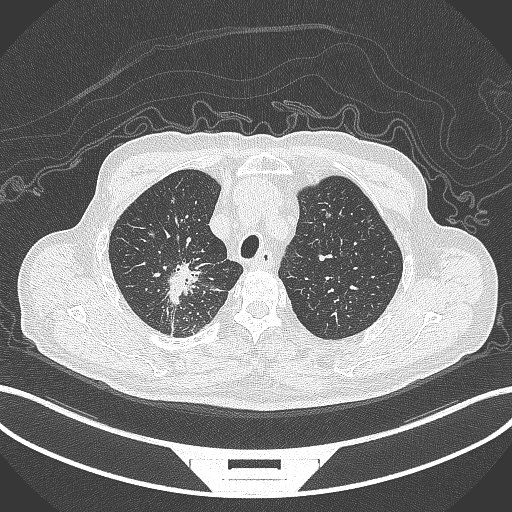
Chest CT, one axial slice; slice 305 of 407 in the series (ordered by position); reconstruction kernel B70f; lung window (W 1500 / L -600 HU); 1 mm slice thickness; 512 × 512 image matrix, field of view 400 × 400 mm. Male patient, age 69 years. Case-level facts recorded for this patient, not image findings: clinical TNM (as recorded): T1c N1 M1.
Annotated regions visible in this slice (rectangle marked by the reading radiologist):
- lung tumour (recorded histology: adenocarcinoma): bounding box (x1, y1, x2, y2) in pixels: (165, 259, 207, 310)